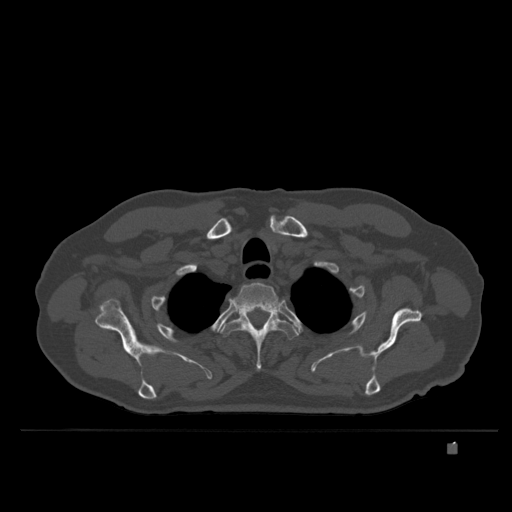
CT including the spine, one axial slice; position 305 of 435 along the scan axis; bone window (W 1800 / L 400 HU); 1.5 mm slice thickness; 512 × 512 image matrix, field of view 434 × 434 mm. Patient: male, 73 years. From the clinical record (not read from this slice): primary cancer: skin.
Outlined on this slice (semi-automatically segmented with operator editing):
- T2 vertebra: bounding box <229,283,282,311> (left, top, right, bottom; pixels)
- T3 vertebra: <219,308,299,371>